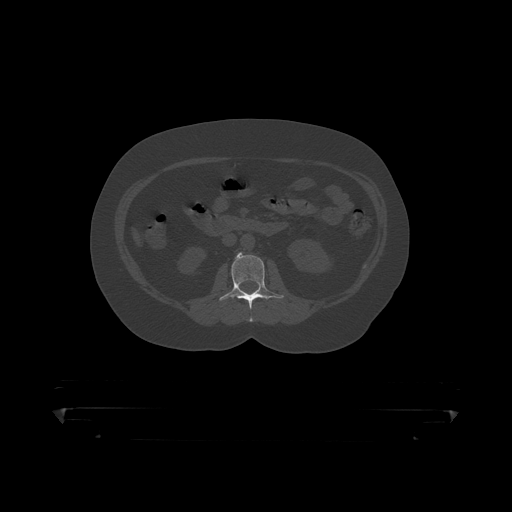
CT including the spine, one axial slice. Slice 117 of 390 in the series (ordered by position). Reconstruction kernel STANDARD. 120 kVp. Bone window (W 1800 / L 400 HU). 1.25 mm slice thickness. 512 × 512 image matrix. Male patient, age 60 years. From the clinical record (not read from this slice): primary cancer: prostate.
Structures marked on this image (semi-automatic segmentation, software-assisted and operator-edited):
- L2 vertebra: bounding box <219,253,284,319> (left, top, right, bottom; pixels)